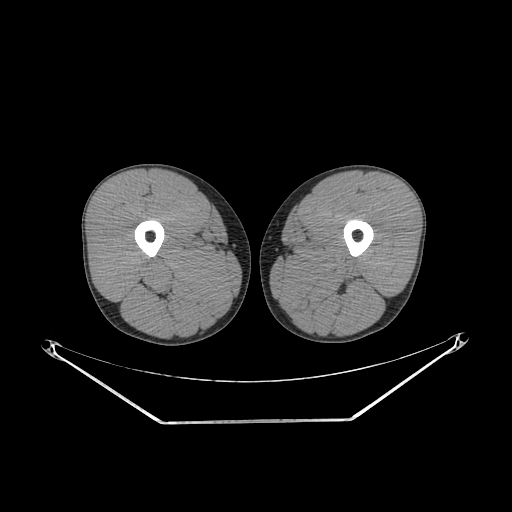
CT of an extremity soft-tissue mass (from a PET/CT study), one axial slice. Position 226 of 267 along the scan axis. 140 kVp. Soft-tissue window (W 400 / L 40 HU). 3.75 mm slice thickness. 512 × 512 image matrix, field of view 500 × 500 mm. Male patient. From the clinical record (not read from this slice): histological type: extraskeletal osteosarcoma; grade: high; site of the primary tumour: left adductur.
Annotated regions visible in this slice (expert contour drawn on MRI and transferred to this co-registered scan by the dataset authors):
- gross tumour volume (mass): bounding box (x1, y1, x2, y2) in pixels: (278, 246, 369, 305)